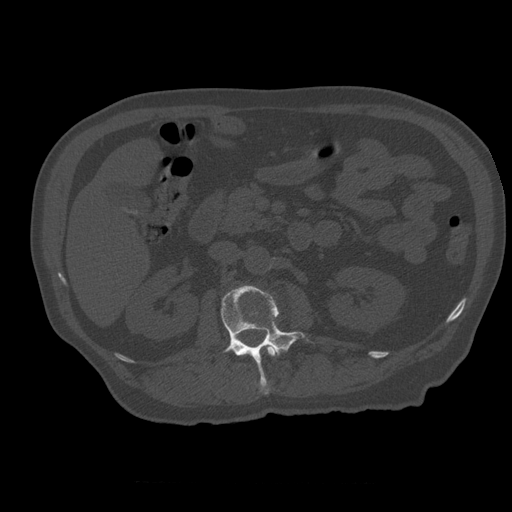
CT including the spine, one axial slice. Slice 216 of 399 in the series (ordered by position). Reconstruction kernel STANDARD. Bone window (W 1800 / L 400 HU). 1.25 mm slice thickness. 512 × 512 image matrix, field of view 407 × 407 mm. Patient age 73 years. From the clinical record (not read from this slice): primary cancer: prostate; vertebrae with lytic lesions (as recorded): L2.
Outlined on this slice (semi-automatically segmented with operator editing):
- L1 vertebra: bounding box [x1, y1, x2, y2] px = [242, 345, 279, 357]
- L2 vertebra: [221, 286, 305, 394]